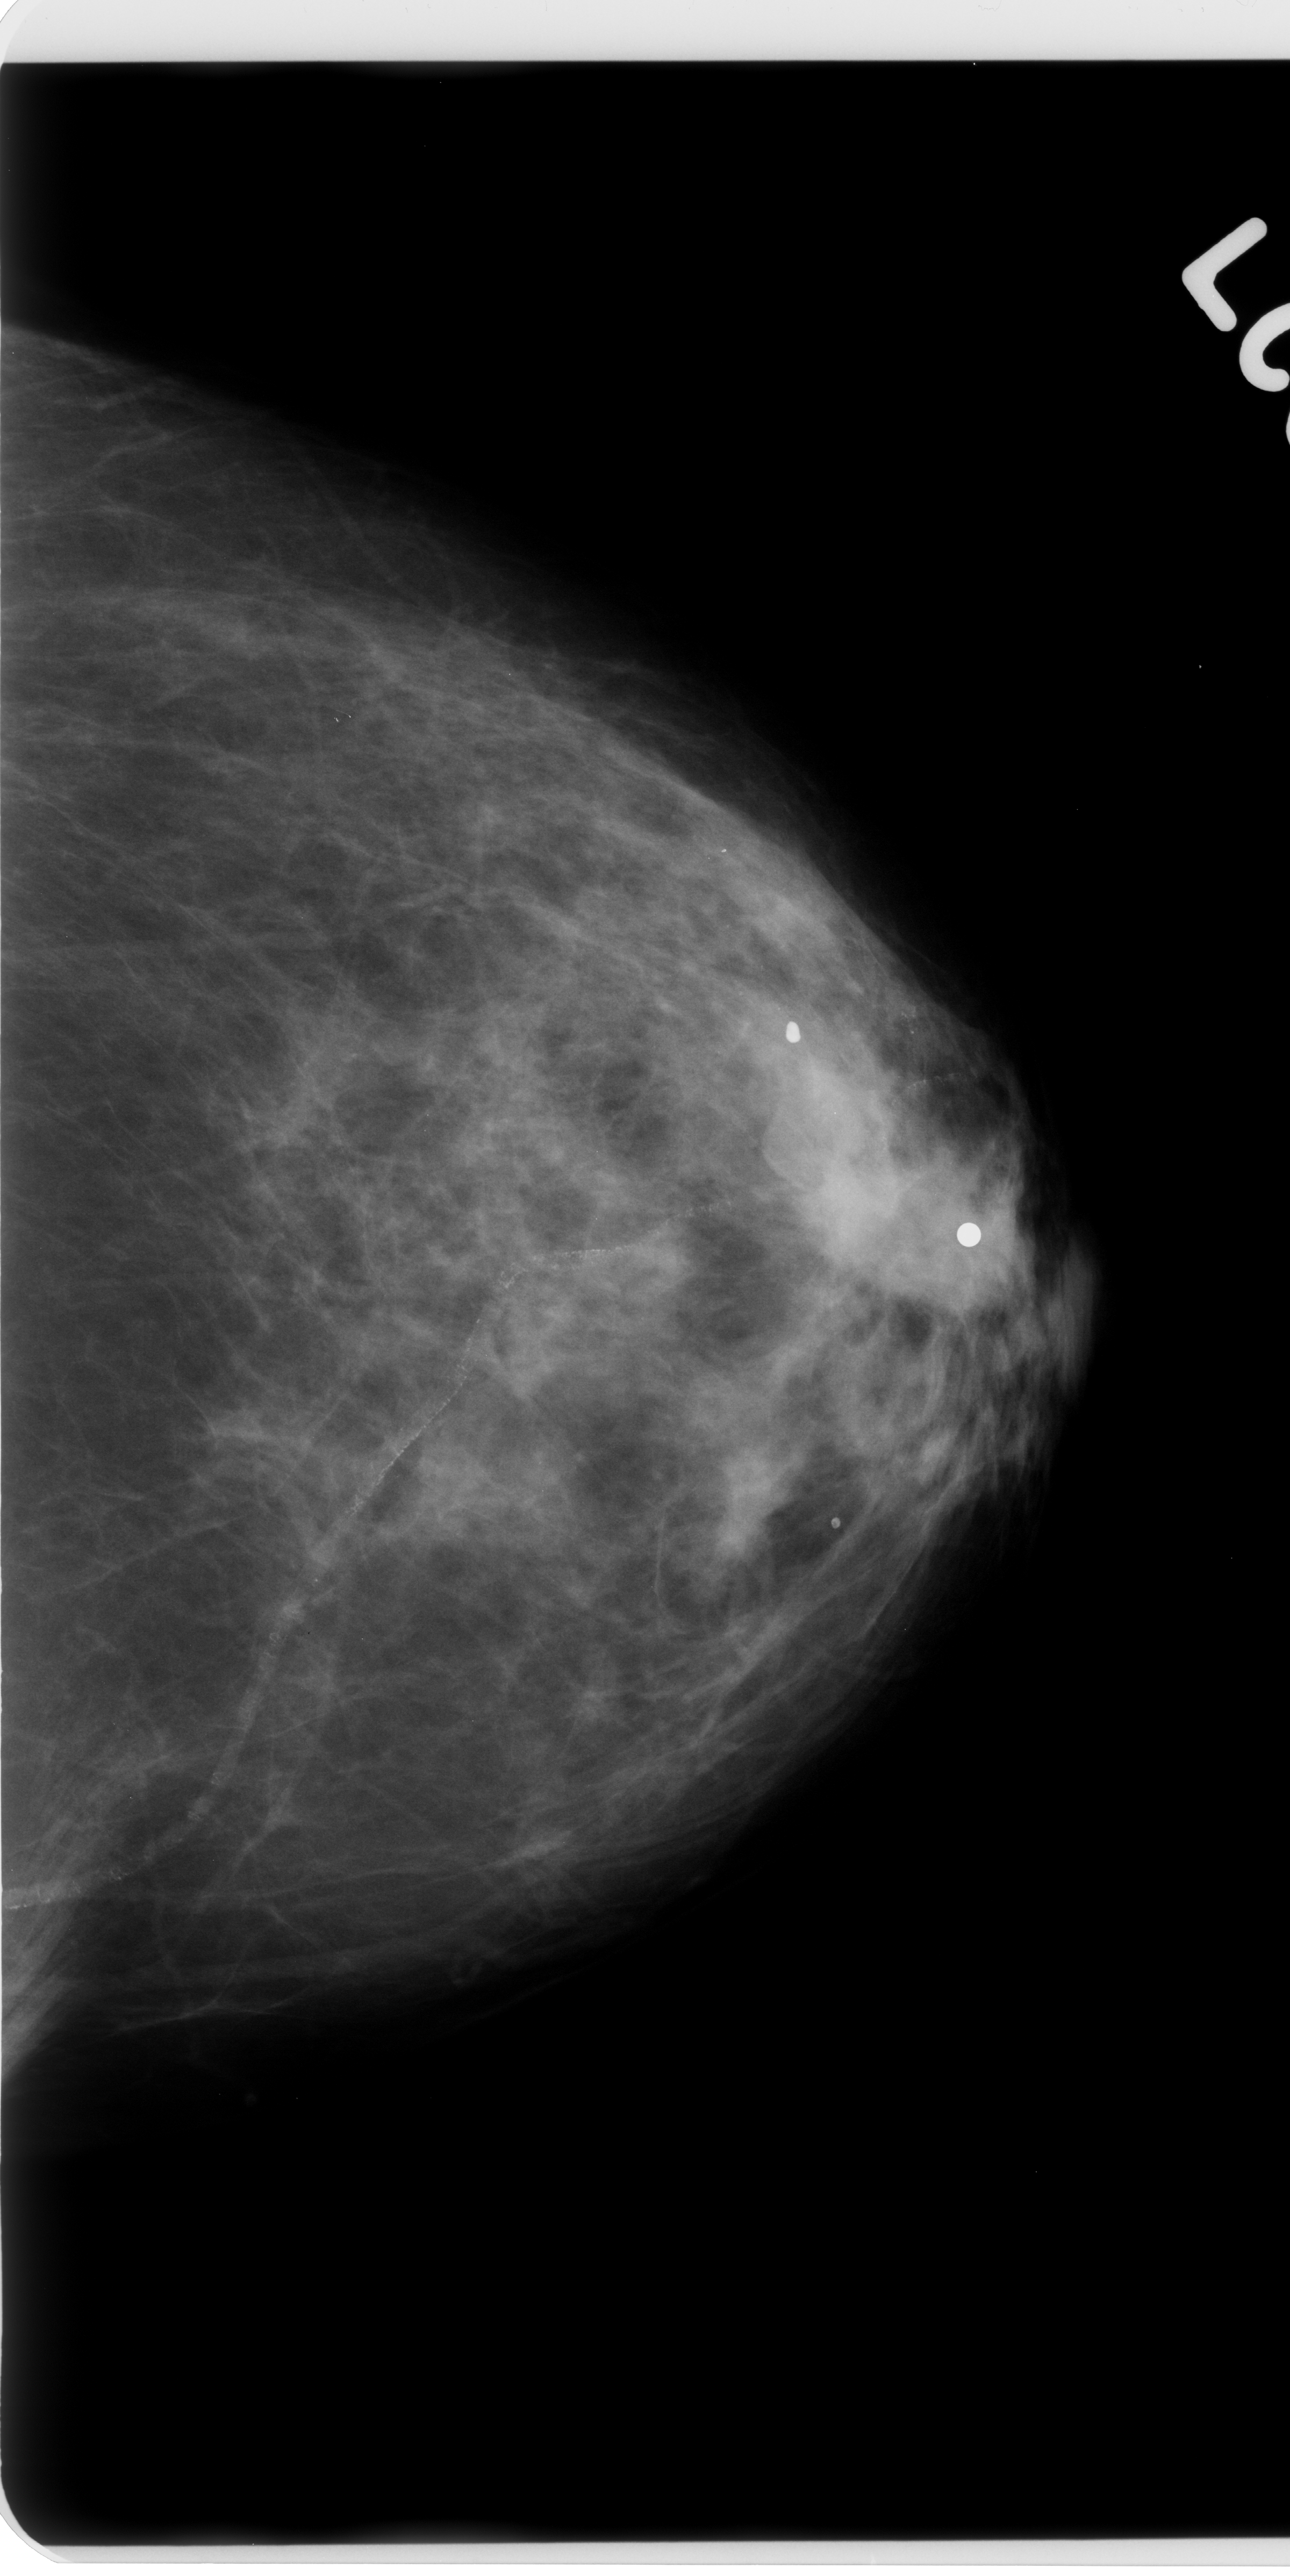
Mammogram (digitized film); left breast; craniocaudal (CC) view.
- Radiologist-marked abnormalities on this image: mass, shape irregular, margins spiculated; BI-RADS assessment category 4; subtlety rating 5 on a 1 (subtle) to 5 (obvious) scale; pathology result (as recorded, not read from the image): malignant.